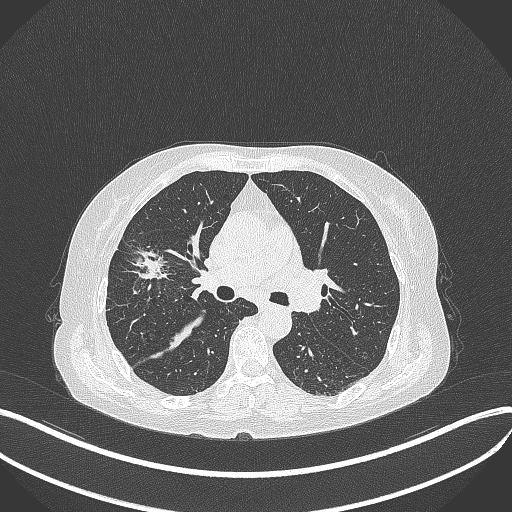
Chest CT, one axial slice; slice 240 of 429 in the series (ordered by position); reconstruction kernel B70f; lung window (W 1500 / L -600 HU); 1 mm slice thickness; 512 × 512 image matrix, field of view 400 × 400 mm. Female patient, age 69 years. Case-level facts recorded for this patient, not image findings: clinical TNM (as recorded): T1b N3 M0.
Structures marked on this image (bounding box drawn by a radiologist):
- lung tumour (recorded histology: small cell carcinoma): bounding box <119,239,176,291> (left, top, right, bottom; pixels)